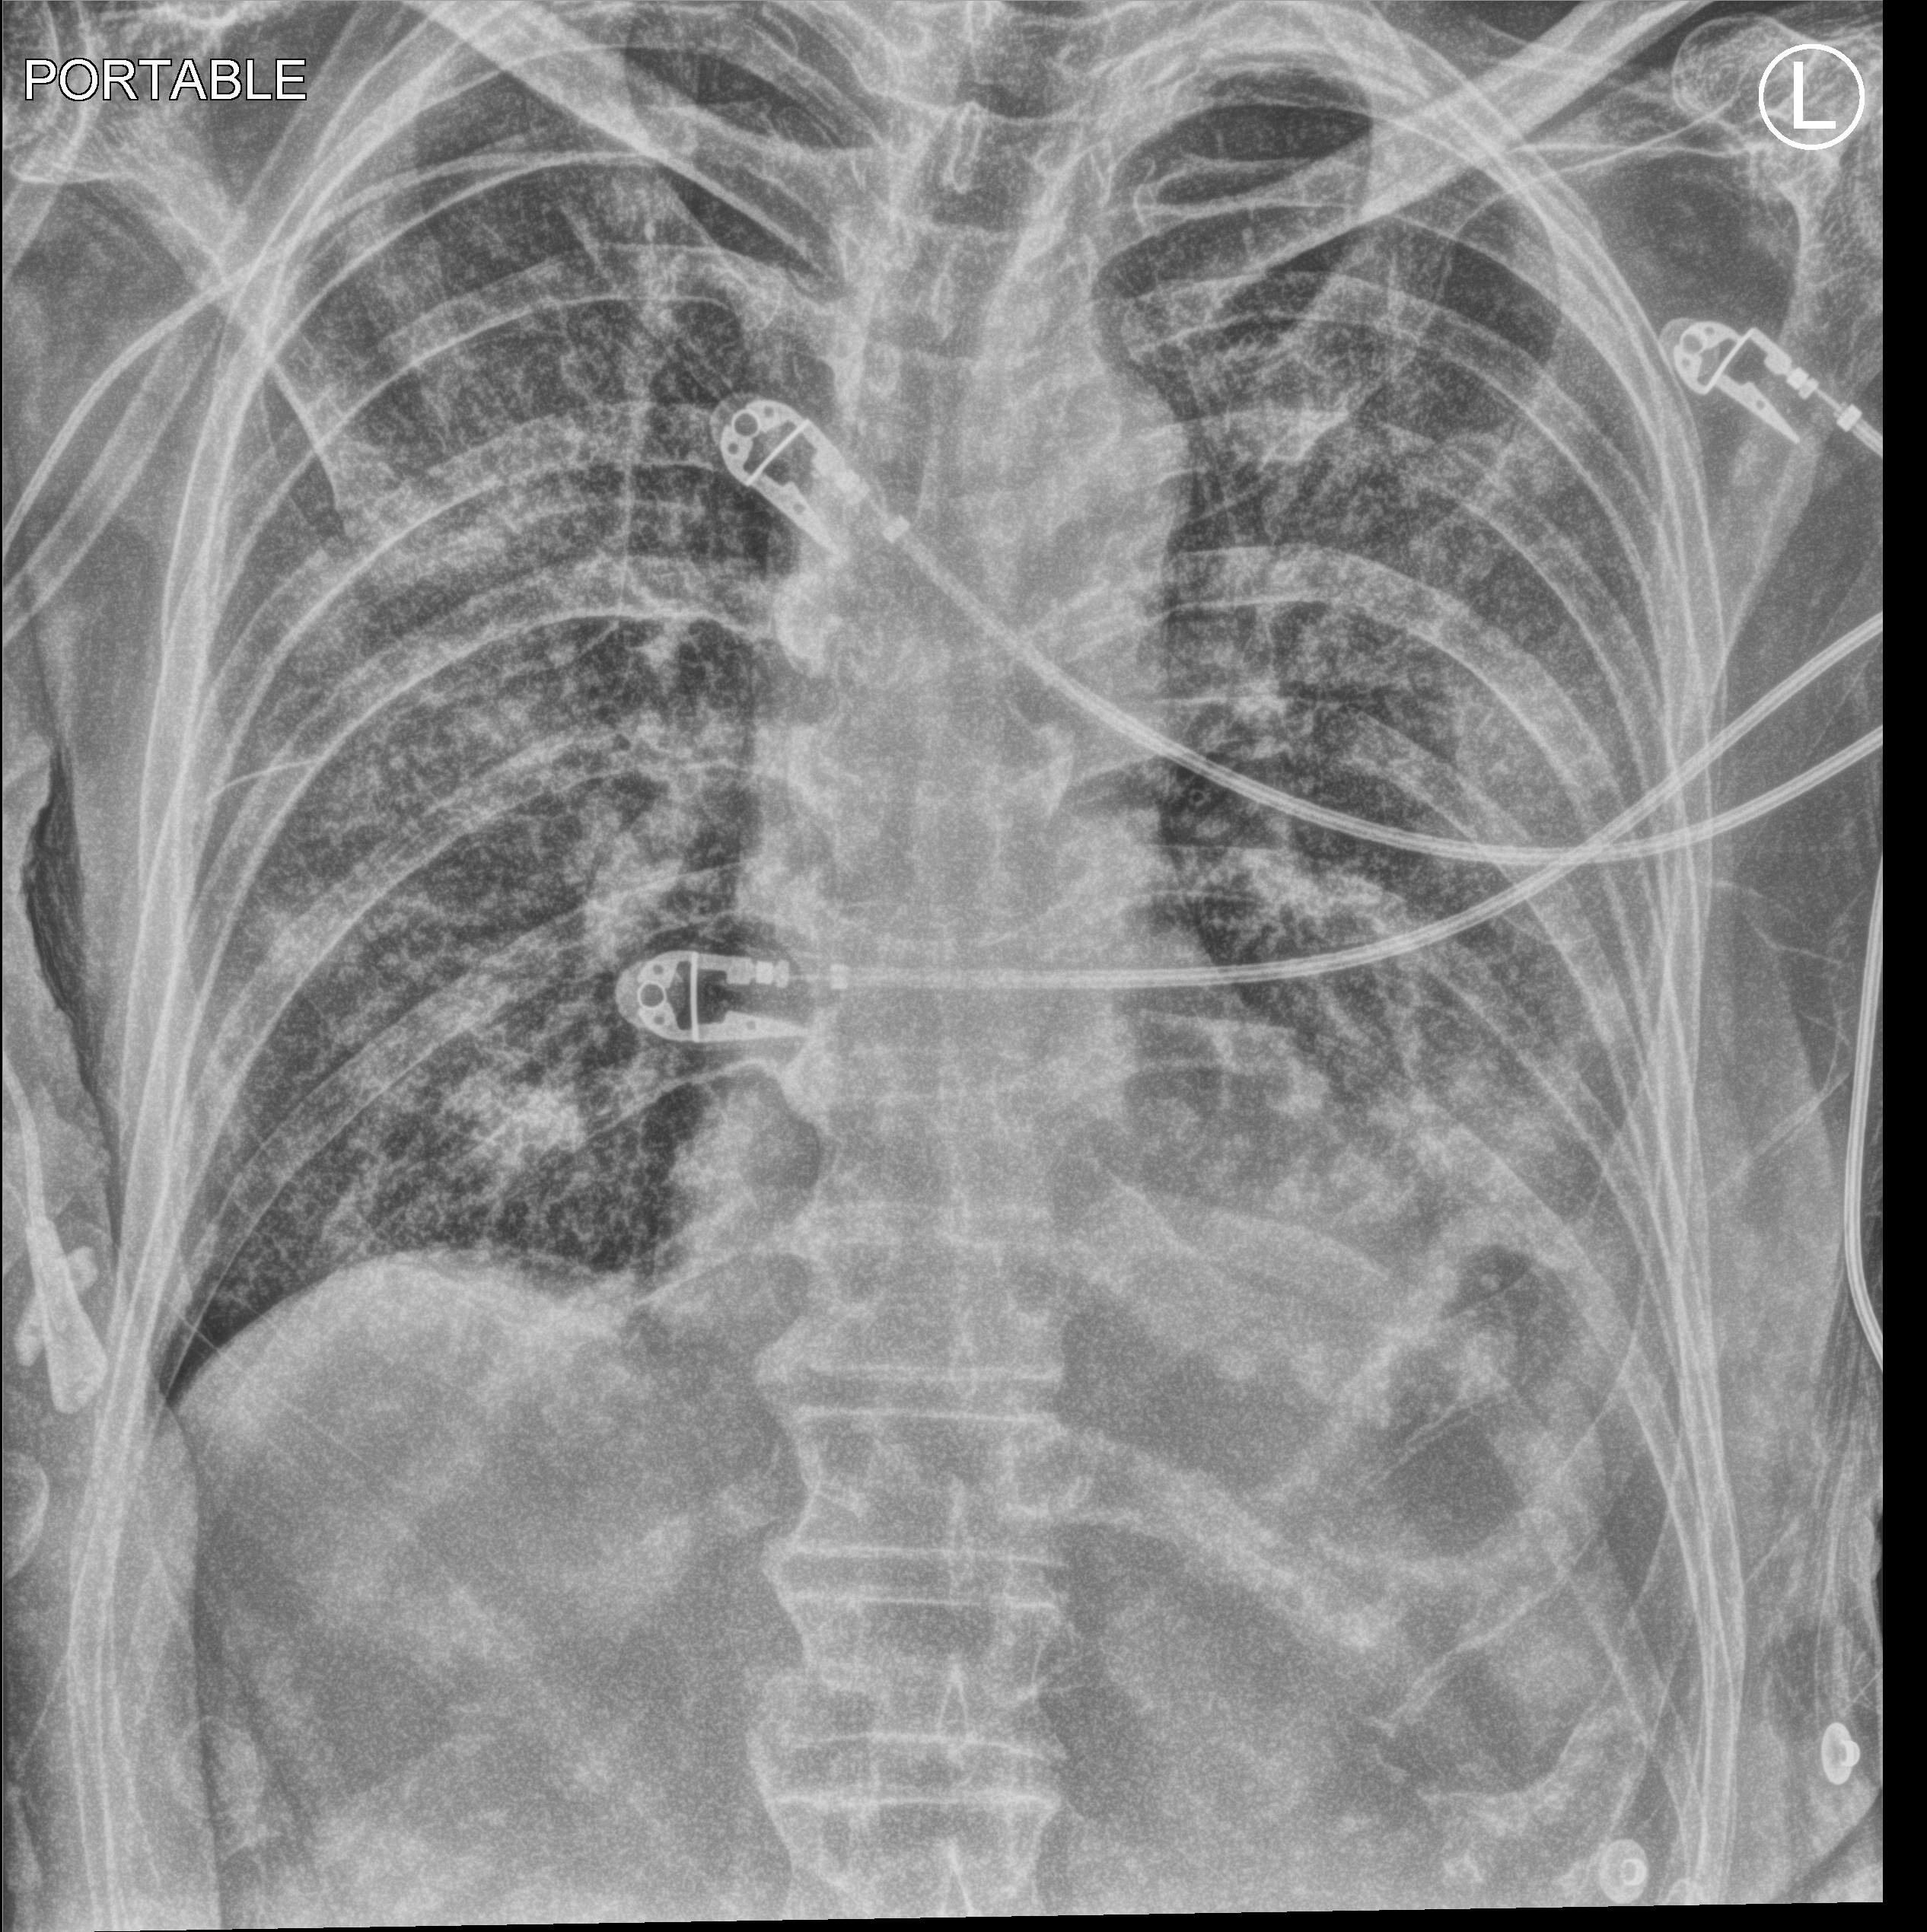
Bedside chest radiograph (computed radiography), anteroposterior (AP) projection. Patient hospitalised with COVID-19; male, aged 60–74 years.
Admission-level facts for this patient (not findings on this image; timing relative to this image not recorded):
- length of hospital stay: 42 days